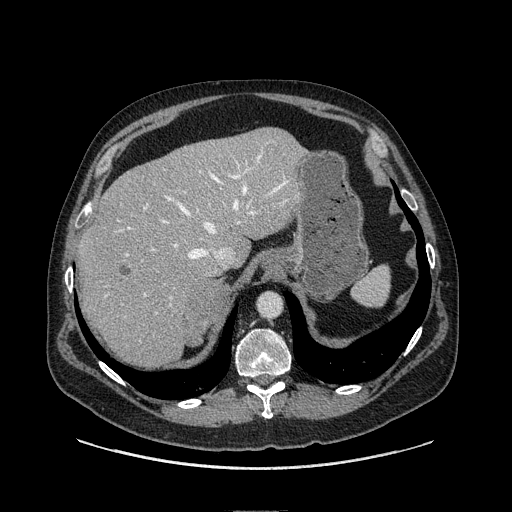
Contrast-enhanced abdominal CT, one axial slice. Position 87 of 149 along the scan axis. Soft-tissue window (W 400 / L 40 HU). 512 × 512 image matrix, field of view 440 × 440 mm. Male patient. Case-level facts recorded for this patient, not image findings: diagnosis: adrenocortical carcinoma; tumour side: right adrenal; tumour size at pathology: 7.5 cm; Ki-67 index: 15 %; stage (as recorded): 2.
Outlined on this slice (semi-automatic segmentation, software-assisted and operator-edited):
- mass: bounding box (x1, y1, x2, y2) in pixels: (187, 279, 228, 343)